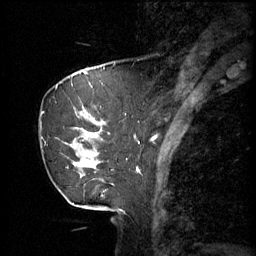
Breast MRI (dynamic contrast-enhanced), one sagittal slice; slice 16 of 60 in the series (ordered by position); 3 images stored at this slice position (order not interpretable as contrast timing); 1.5 T; TE 4.2 ms, TR 11 ms; 256 × 256 image matrix, field of view 220 × 220 mm. Female patient, age 69 years.
Outlined on this slice (semi-automatically segmented with operator editing):
- analysis volume of interest (the breast-tissue region the enhancement analysis was run in; not a lesion): box from (x=42, y=88) to (x=116, y=189) px
- tumour enhancement mask (voxels above the 70 % enhancement threshold inside the analysis volume of interest): (x=75, y=112)–(x=102, y=177)